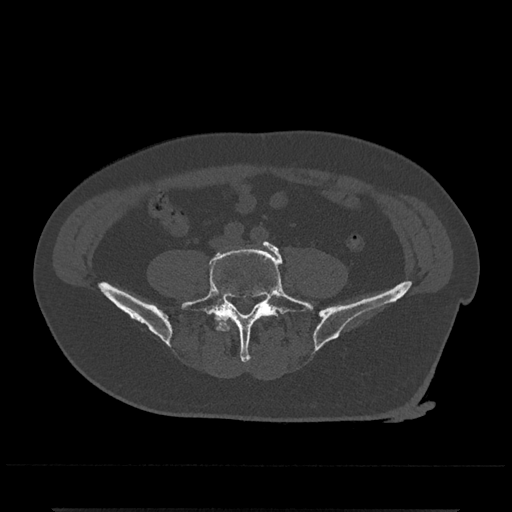
CT including the spine, one axial slice. Position 94 of 797 along the scan axis. Reconstruction kernel Br40s/3. 120 kVp. Bone window (W 1800 / L 400 HU). 0.5 mm slice thickness. 512 × 512 image matrix. Male patient, age 67 years. From the clinical record (not read from this slice): primary cancer: prostate.
Annotated regions visible in this slice (semi-automatic segmentation, software-assisted and operator-edited):
- L4 vertebra: box from (x=220, y=321) to (x=230, y=331) px
- L5 vertebra: (x=181, y=241)–(x=314, y=363)